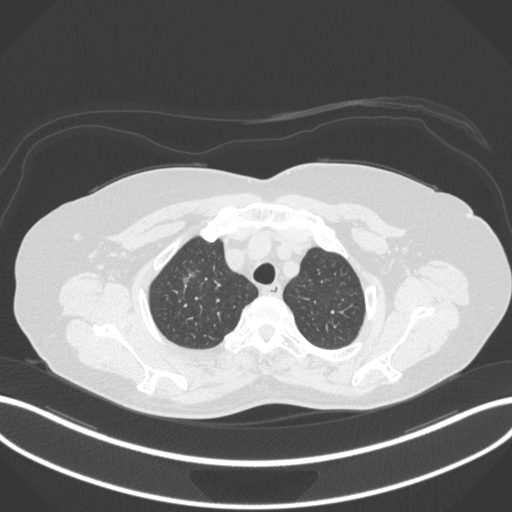
Chest CT, one axial slice; position 296 of 365 along the scan axis; reconstruction kernel B31f; lung window (W 1500 / L -600 HU); 1 mm slice thickness; 512 × 512 image matrix. Patient: female, 62 years. Case-level facts recorded for this patient, not image findings: clinical TNM (as recorded): T1c N0 M0.
Structures marked on this image (rectangle marked by the reading radiologist):
- lung tumour (recorded histology: adenocarcinoma): box from (x=172, y=255) to (x=209, y=296) px